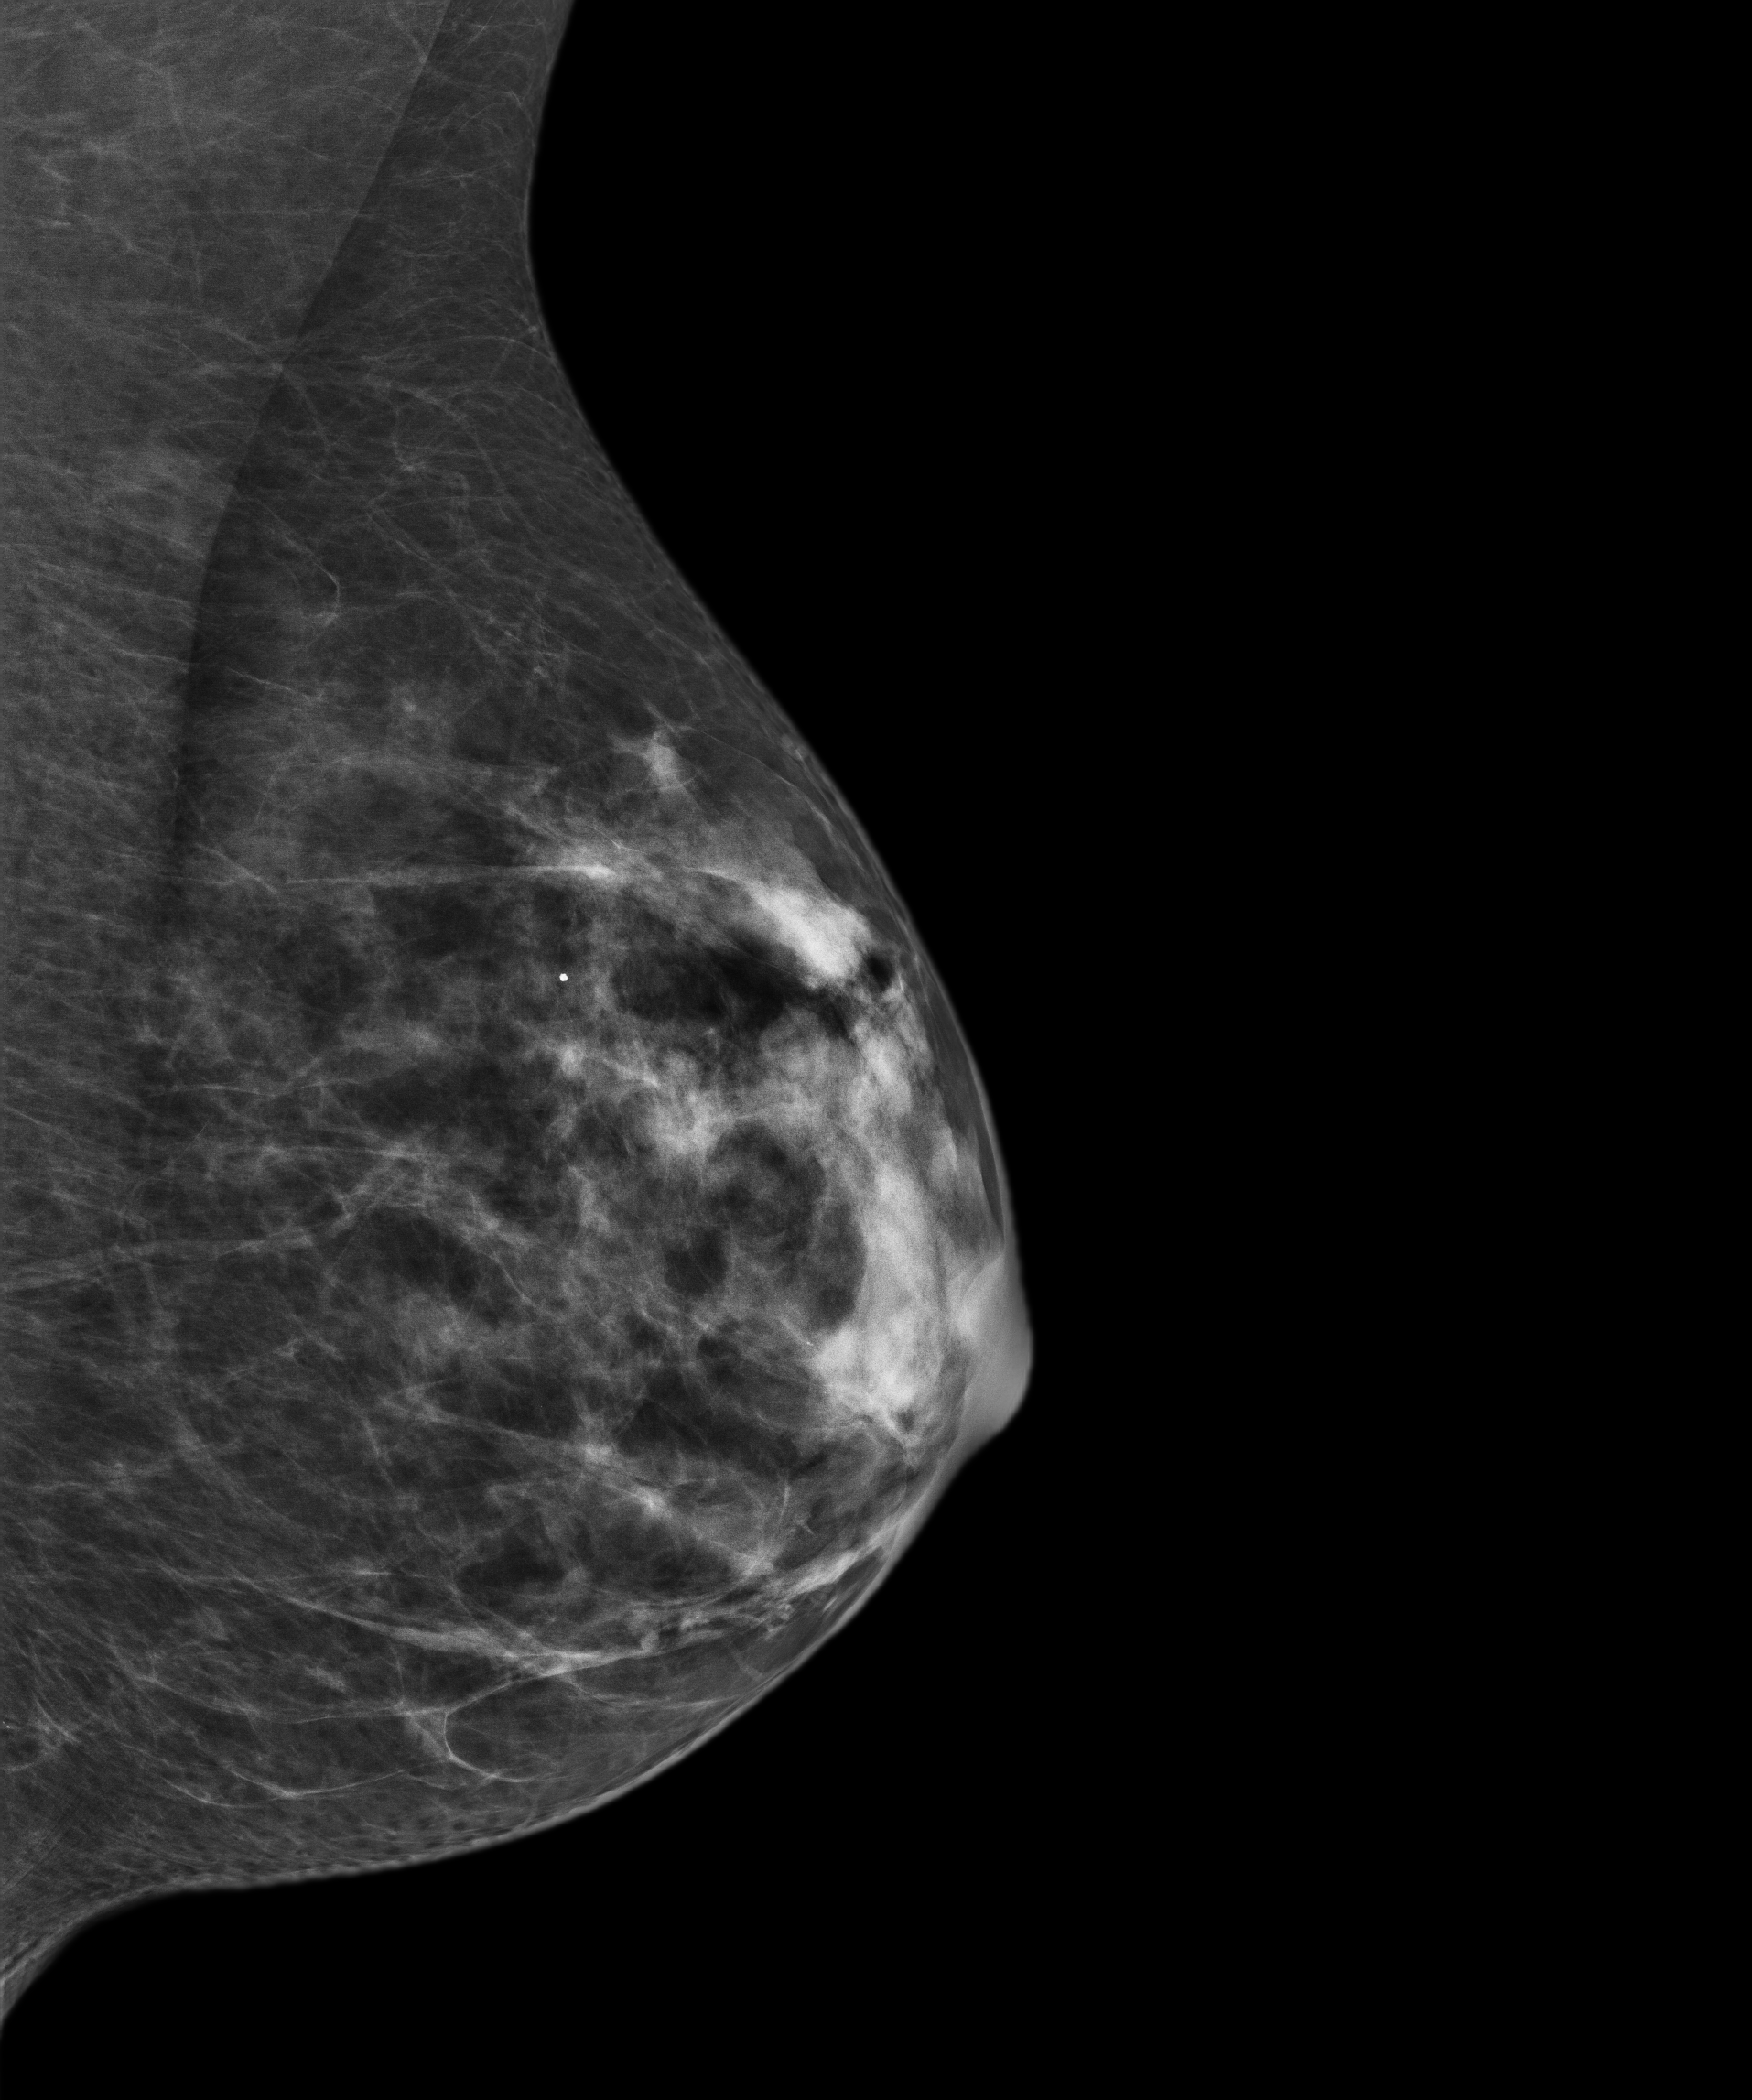
Digital mammogram (FFDM), left breast, medio-lateral oblique projection, screening examination, compressed breast thickness 28.7 mm. Patient: female, 43 years.
Final BI-RADS assessment for this screening round (tomosynthesis exam, both breasts): category 1.